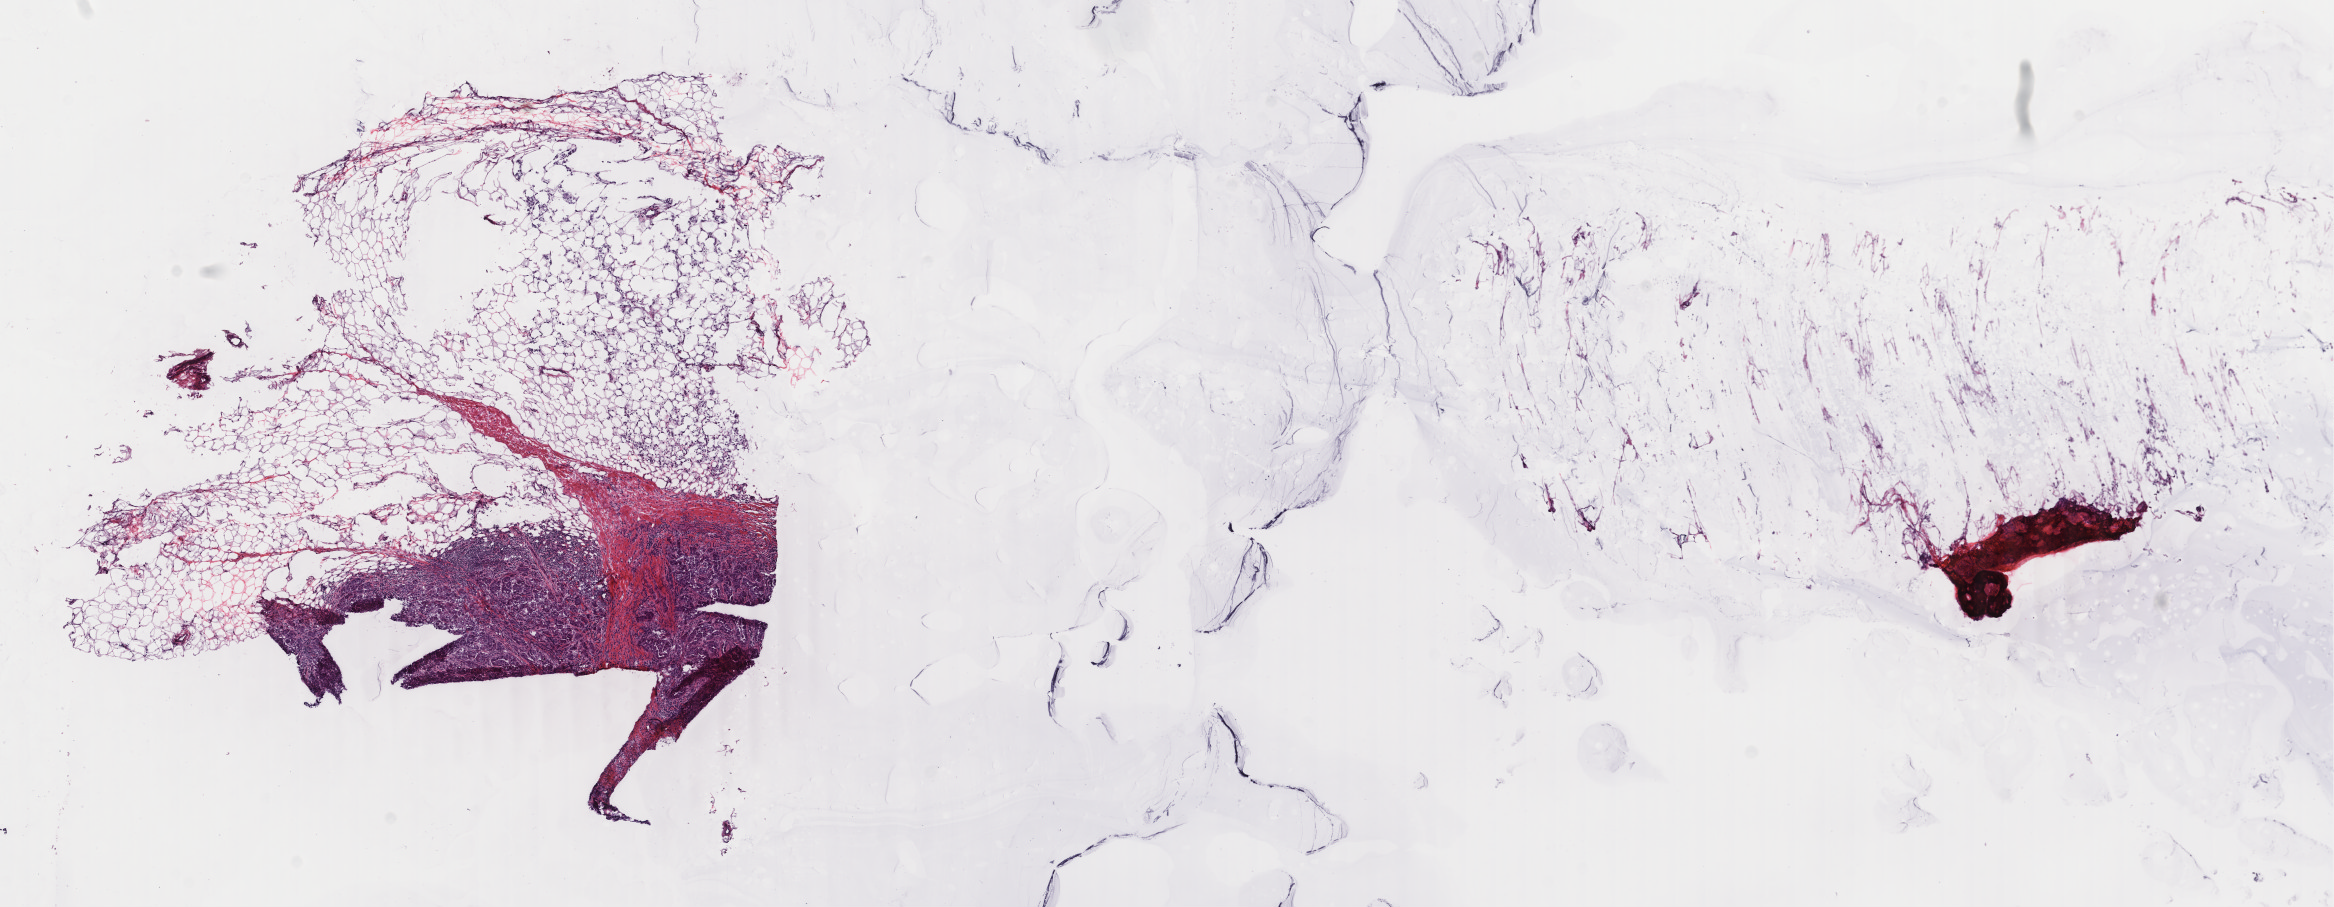
H&E whole-slide image — a low-resolution overview of the entire scanned area, about 18.6 x 7.2 mm (acquisition: 40x scan). Frozen section from the top of the tissue portion. Primary tumour sample from the breast. Female patient; age at initial diagnosis 47 years. Composition of this section per pathologist review: tumour cells 25%, tumour nuclei 85%, normal cells 0%, stromal cells 75%, necrosis 0%. Infiltration values recorded for this section: lymphocyte infiltration 3%, monocyte infiltration 0%, neutrophil infiltration 0%.
AJCC pathologic stage: IIA (6th edition). Histologic diagnosis: Infiltrating duct carcinoma, NOS. Lymph nodes positive (case pathology): 2 of 25 examined. Laterality: left.